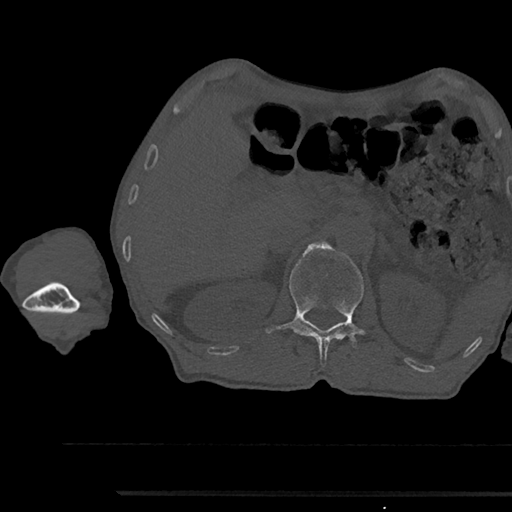
CT including the spine, one axial slice; position 639 of 797 along the scan axis; reconstruction kernel Br40s/3; bone window (W 1800 / L 400 HU); 0.5 mm slice thickness; 512 × 512 image matrix, field of view 367 × 367 mm. Patient: male, 79 years. Case-level facts recorded for this patient, not image findings: primary cancer: prostate.
Structures marked on this image (semi-automatically segmented with operator editing):
- L1 vertebra: bounding box <267,241,365,362> (left, top, right, bottom; pixels)